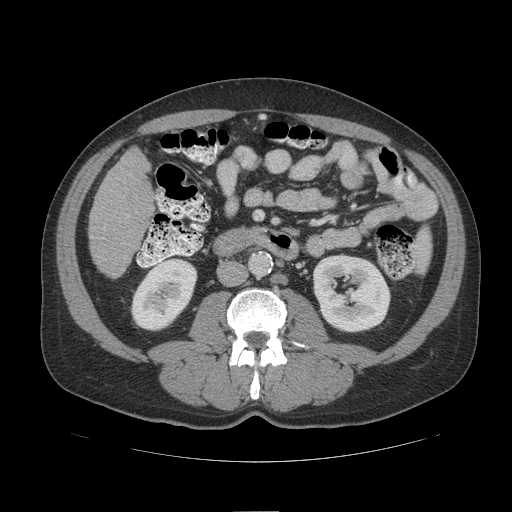
Contrast-enhanced abdominal CT (liver protocol), one axial slice; position 33 of 109 along the scan axis; reconstruction kernel STANDARD; 140 kVp; soft-tissue window (W 400 / L 40 HU); 2.5 mm slice thickness; 512 × 512 image matrix, field of view 420 × 420 mm. Case-level facts recorded for this patient, not image findings: diagnosis: hepatocellular carcinoma (patient treated with transarterial chemoembolisation; whether this scan precedes or follows treatment is not stated here); TNM stage (as recorded): Stage-IIIB.
Annotated regions visible in this slice (semi-automatically segmented with operator editing):
- liver parenchyma outside the tumour (the mass and vessels are separate outlines, so this box may not span the whole liver): bounding box (x1, y1, x2, y2) in pixels: (90, 148, 152, 278)